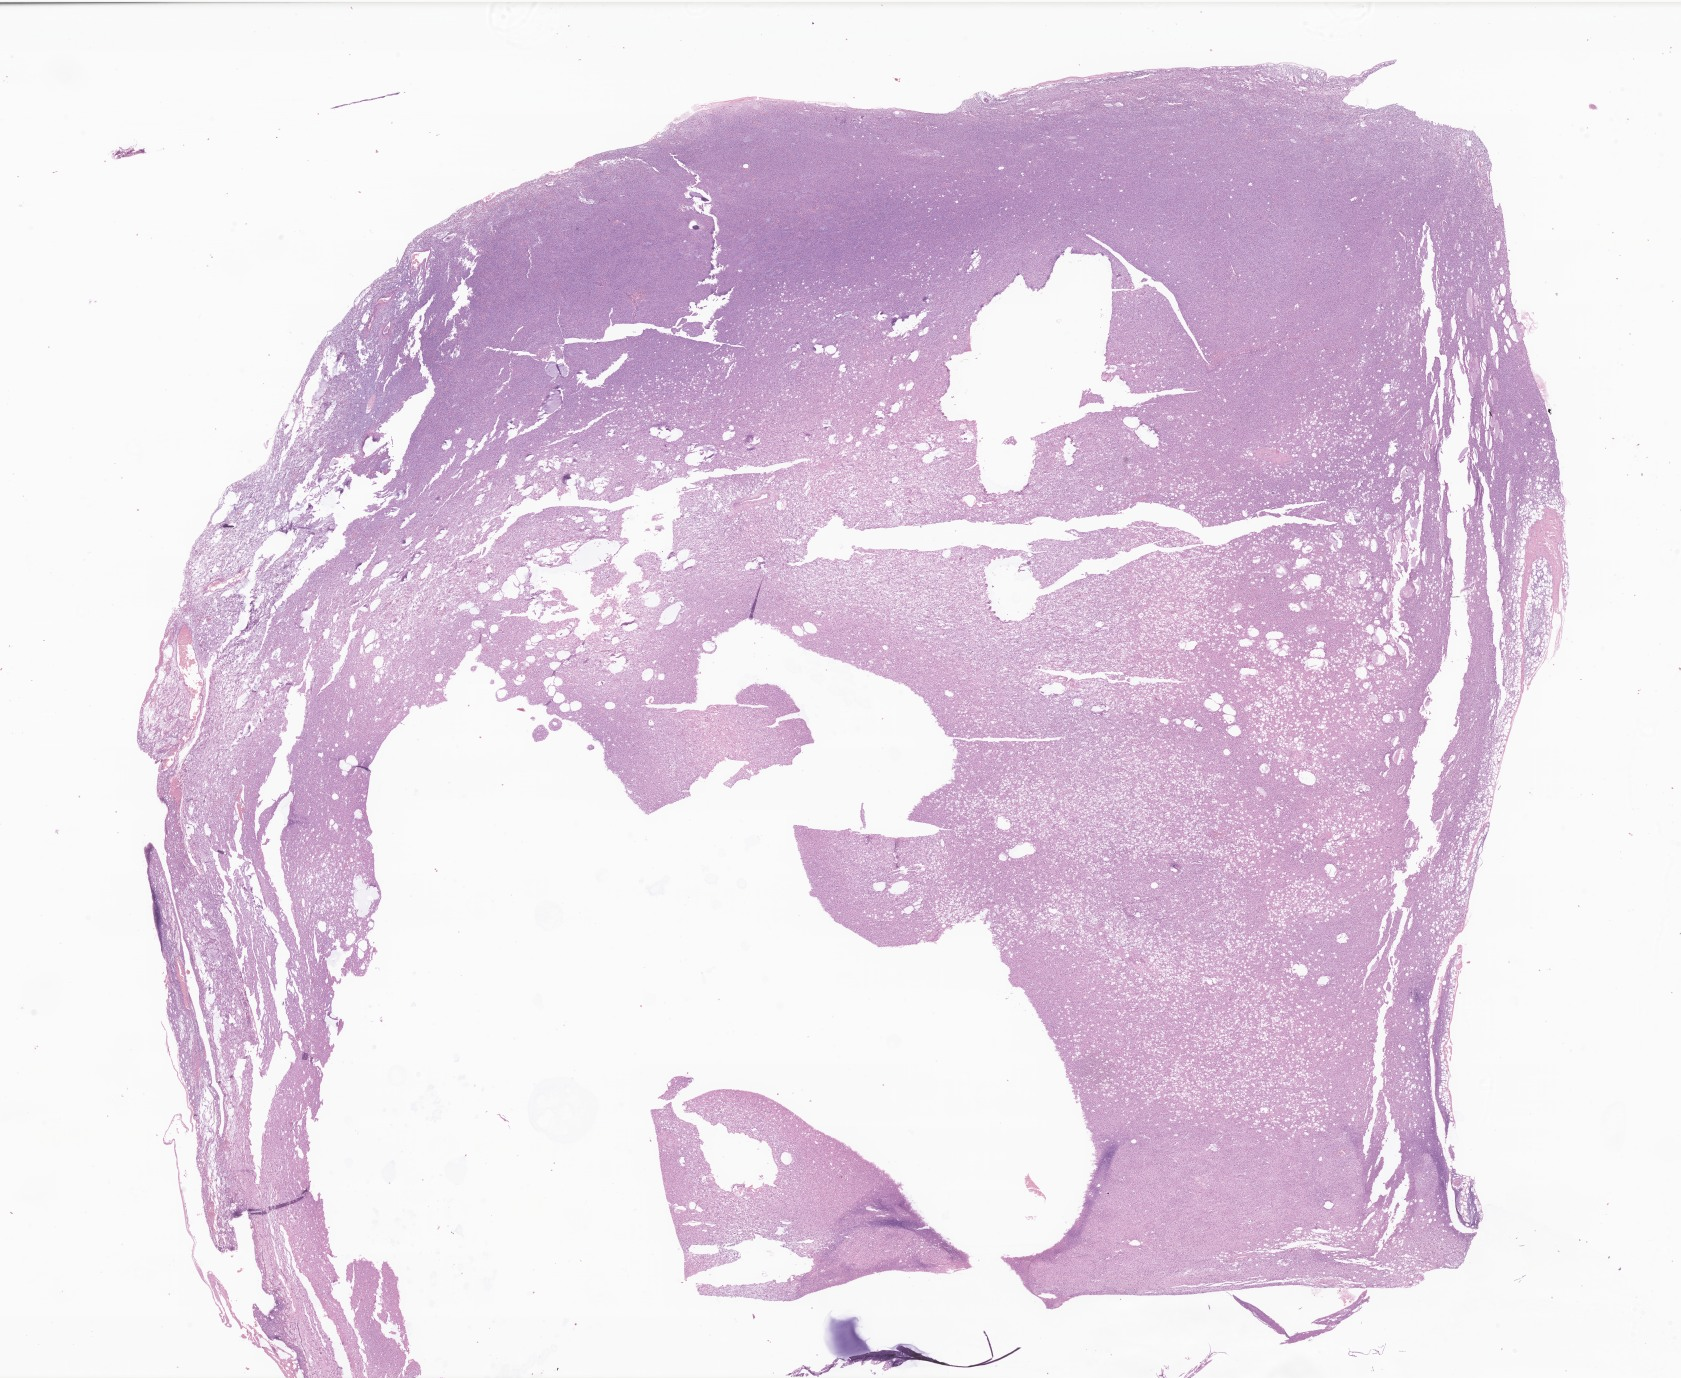
Hematoxylin and eosin (H&E) whole-slide image of tumor tissue from the soft tissue — shown as a low-resolution overview of the whole scanned area (about 28.3 x 23.2 mm); FFPE section. Patient male; age 171 months (14 years 3 months).
• recorded diagnosis: Myxoid liposarcoma